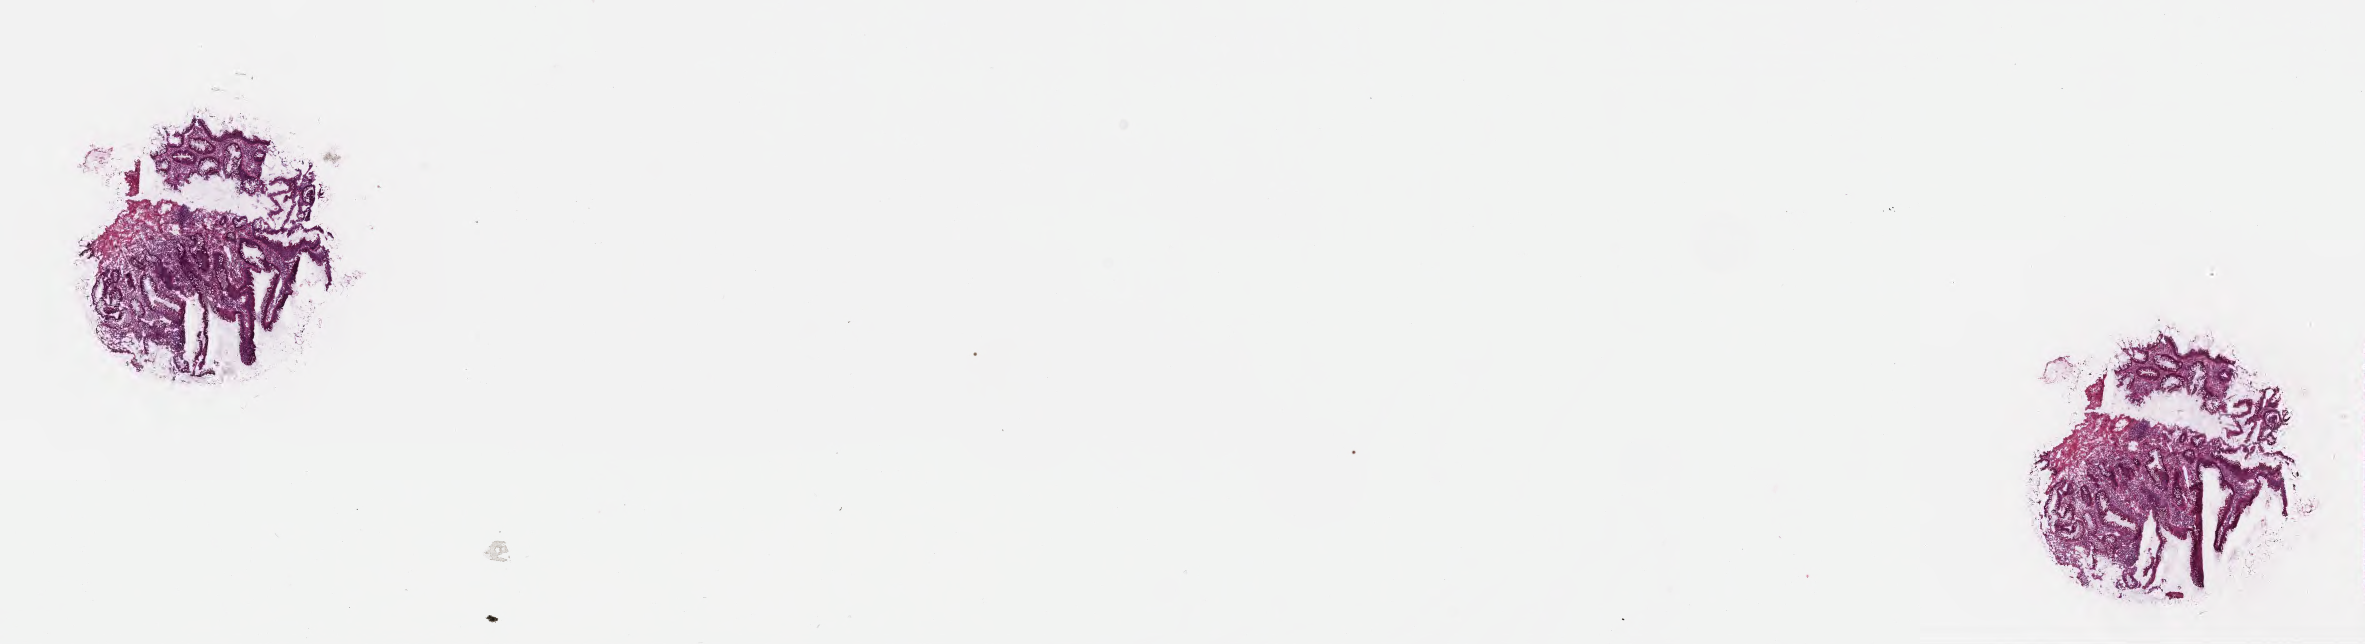
Whole-slide image, H&E stain — whole scanned area (about 19.1 x 5.2 mm) shown as a low-resolution overview; frozen section (tissue freezing medium); specimen: premalignant lesion from a patient with tubulovillous adenoma, NOS; anatomic site: ascending colon. Male patient; age at initial diagnosis 75 years. Slide review estimates, as recorded: tumor cells 80%, tumor nuclei 80%, stromal cells 15%, necrosis 0%, normal cells 5%. Inflammatory infiltration, as recorded: lymphocyte infiltration 4%, monocyte infiltration 1%, neutrophil infiltration 4%.
This section: sample classed premalignant; the patient's recorded diagnosis is given above.